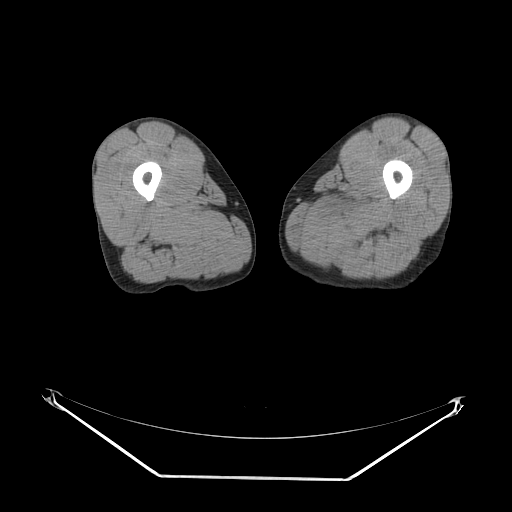
CT of an extremity soft-tissue mass (from a PET/CT study), one axial slice. Slice 8 of 267 in the series (ordered by position). Reconstruction kernel SOFT. 140 kVp. Soft-tissue window (W 400 / L 40 HU). 512 × 512 image matrix, field of view 500 × 500 mm. Male patient. From the clinical record (not read from this slice): histological type: pleiomorphic liposarcoma; grade: high; site of the primary tumour: left thigh.
Outlined on this slice (expert contour drawn on MRI and transferred to this co-registered scan by the dataset authors):
- gross tumour volume including surrounding oedema: box from (x=329, y=199) to (x=368, y=232) px